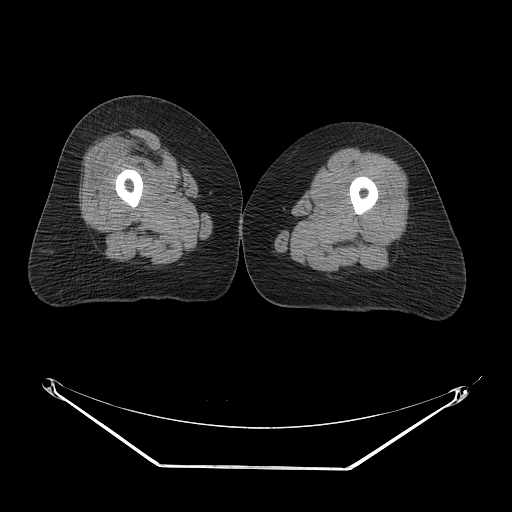
CT of an extremity soft-tissue mass (from a PET/CT study), one axial slice; position 19 of 267 along the scan axis; reconstruction kernel STANDARD; 140 kVp; soft-tissue window (W 400 / L 40 HU); 3.75 mm slice thickness; 512 × 512 image matrix, field of view 500 × 500 mm. Female patient. Case-level facts recorded for this patient, not image findings: histological type: malignant solitary fibrous tumor; grade: intermediate; site of the primary tumour: right thigh.
Outlined on this slice (expert contour drawn on MRI and transferred to this co-registered scan by the dataset authors):
- gross tumour volume including surrounding oedema: bounding box (x1, y1, x2, y2) in pixels: (125, 130, 186, 175)